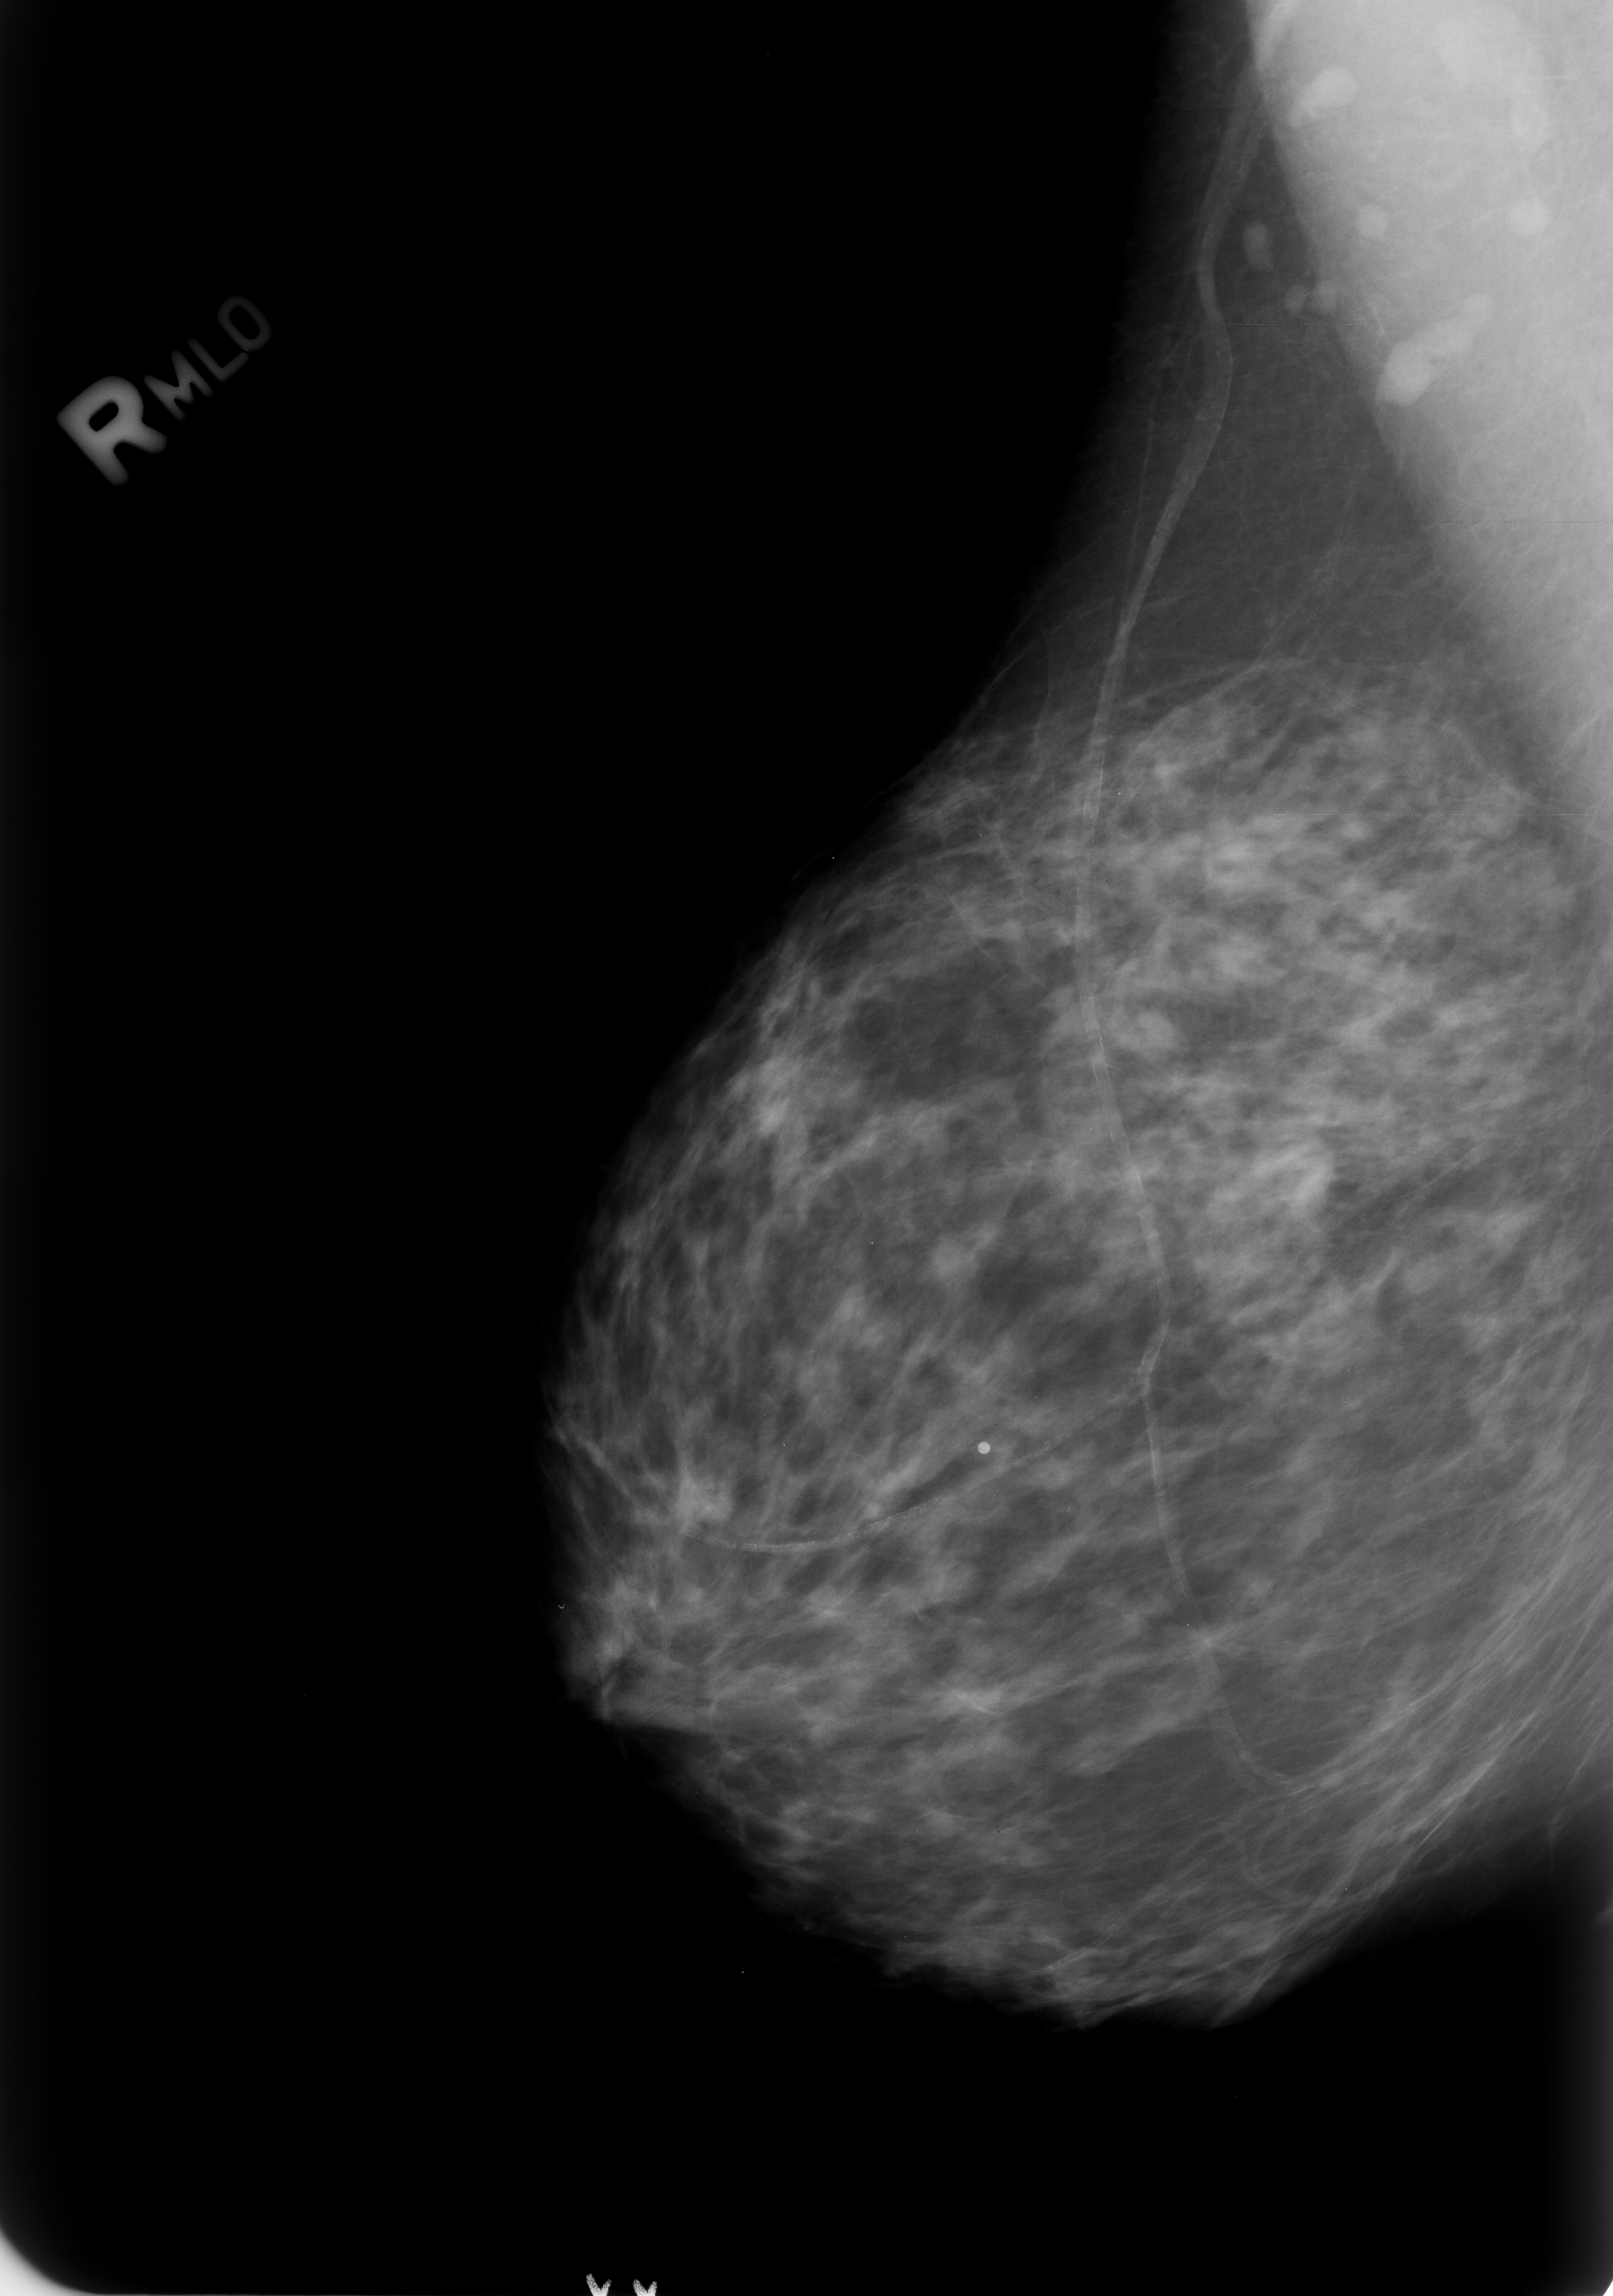
Digitized screen-film mammogram; right breast; mediolateral oblique (MLO) view; breast composition: scattered fibroglandular densities (BI-RADS density category 2 of 4); 1613 × 2296 image matrix.
Expert-marked regions of interest on this image (one box per marked abnormality):
- Finding 1 of 2: calcifications, morphology vascular; BI-RADS assessment category 2; outcome (as recorded, no biopsy): benign without callback (not worked up further): bounding box (x1, y1, x2, y2) in pixels: (672, 248, 1310, 1800)
- Finding 2 of 2: calcifications, morphology lucent center; BI-RADS assessment category 2; outcome (as recorded, no biopsy): benign without callback (not worked up further): (943, 1417, 1016, 1500)